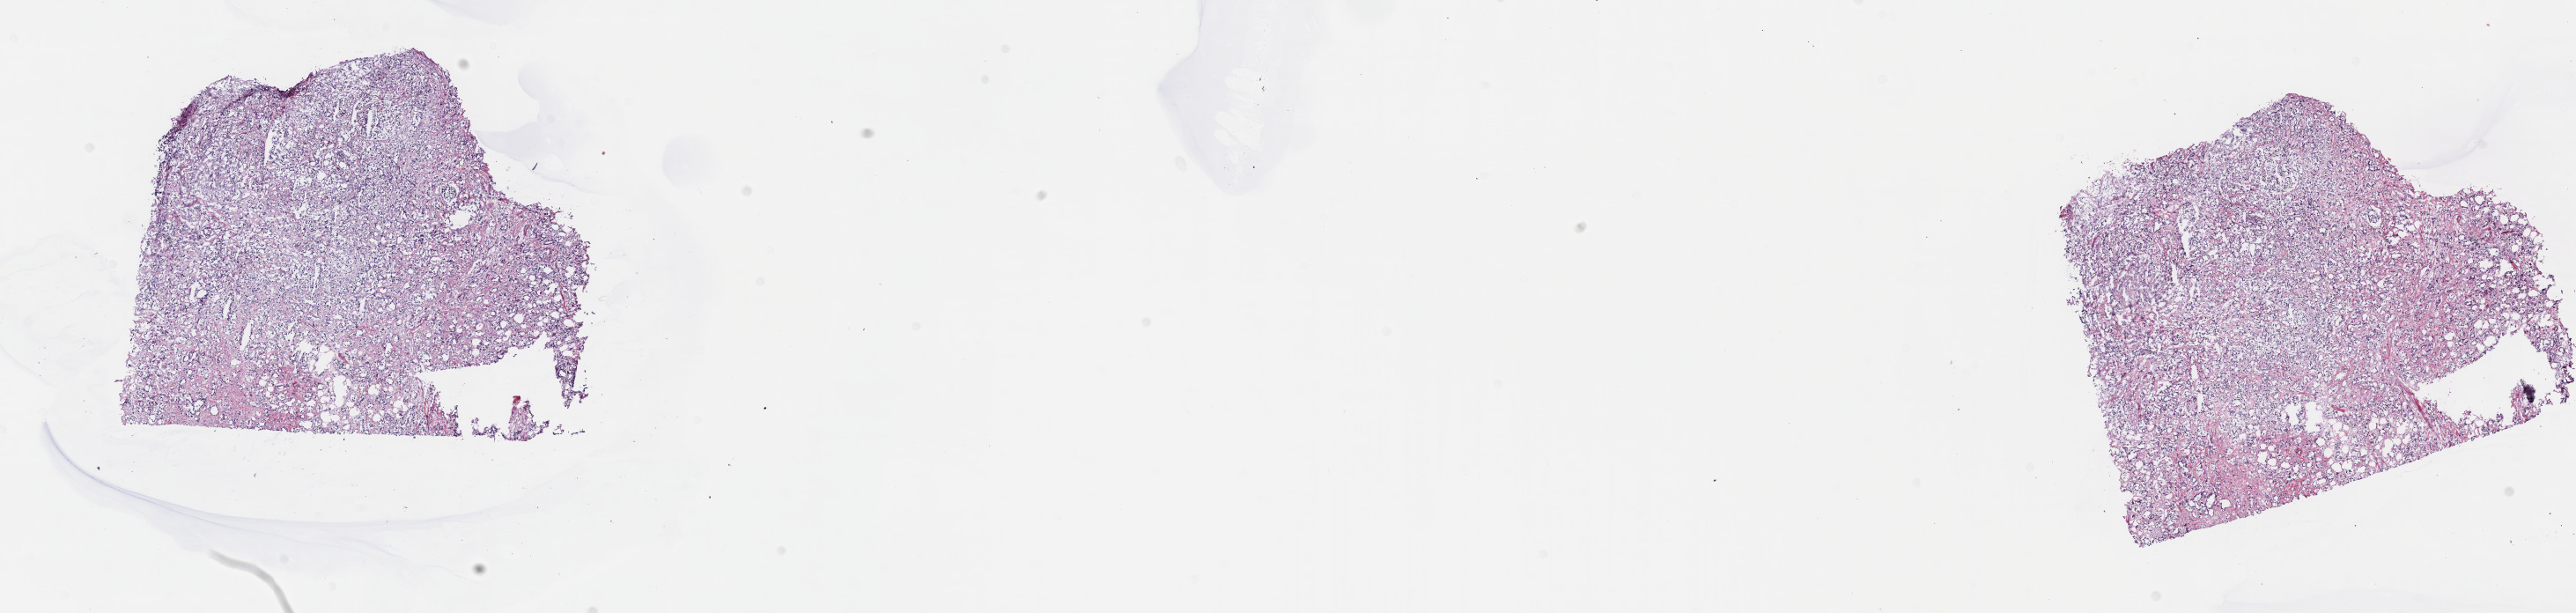
Whole-slide histology image, H&E-stained, whole scanned area (about 23.7 x 5.6 mm) shown as a low-resolution overview. Frozen section from the top of the tissue portion. Sample: primary tumour, pancreas. Patient: male, age at initial diagnosis 54 years. Histologic grade: G3 (poorly differentiated). Pathologist review of this section (percent, as recorded): tumour cells 80%, tumour nuclei 80%, normal cells 0%, stromal cells 20%, necrosis 0%. Inflammatory infiltration, as recorded: lymphocyte infiltration 2%, monocyte infiltration 1%, neutrophil infiltration 5%.
AJCC pathologic stage: IIB (7th edition). Histologic diagnosis: Infiltrating duct carcinoma, NOS. Lymph nodes positive (case pathology): 1 of 12 examined.